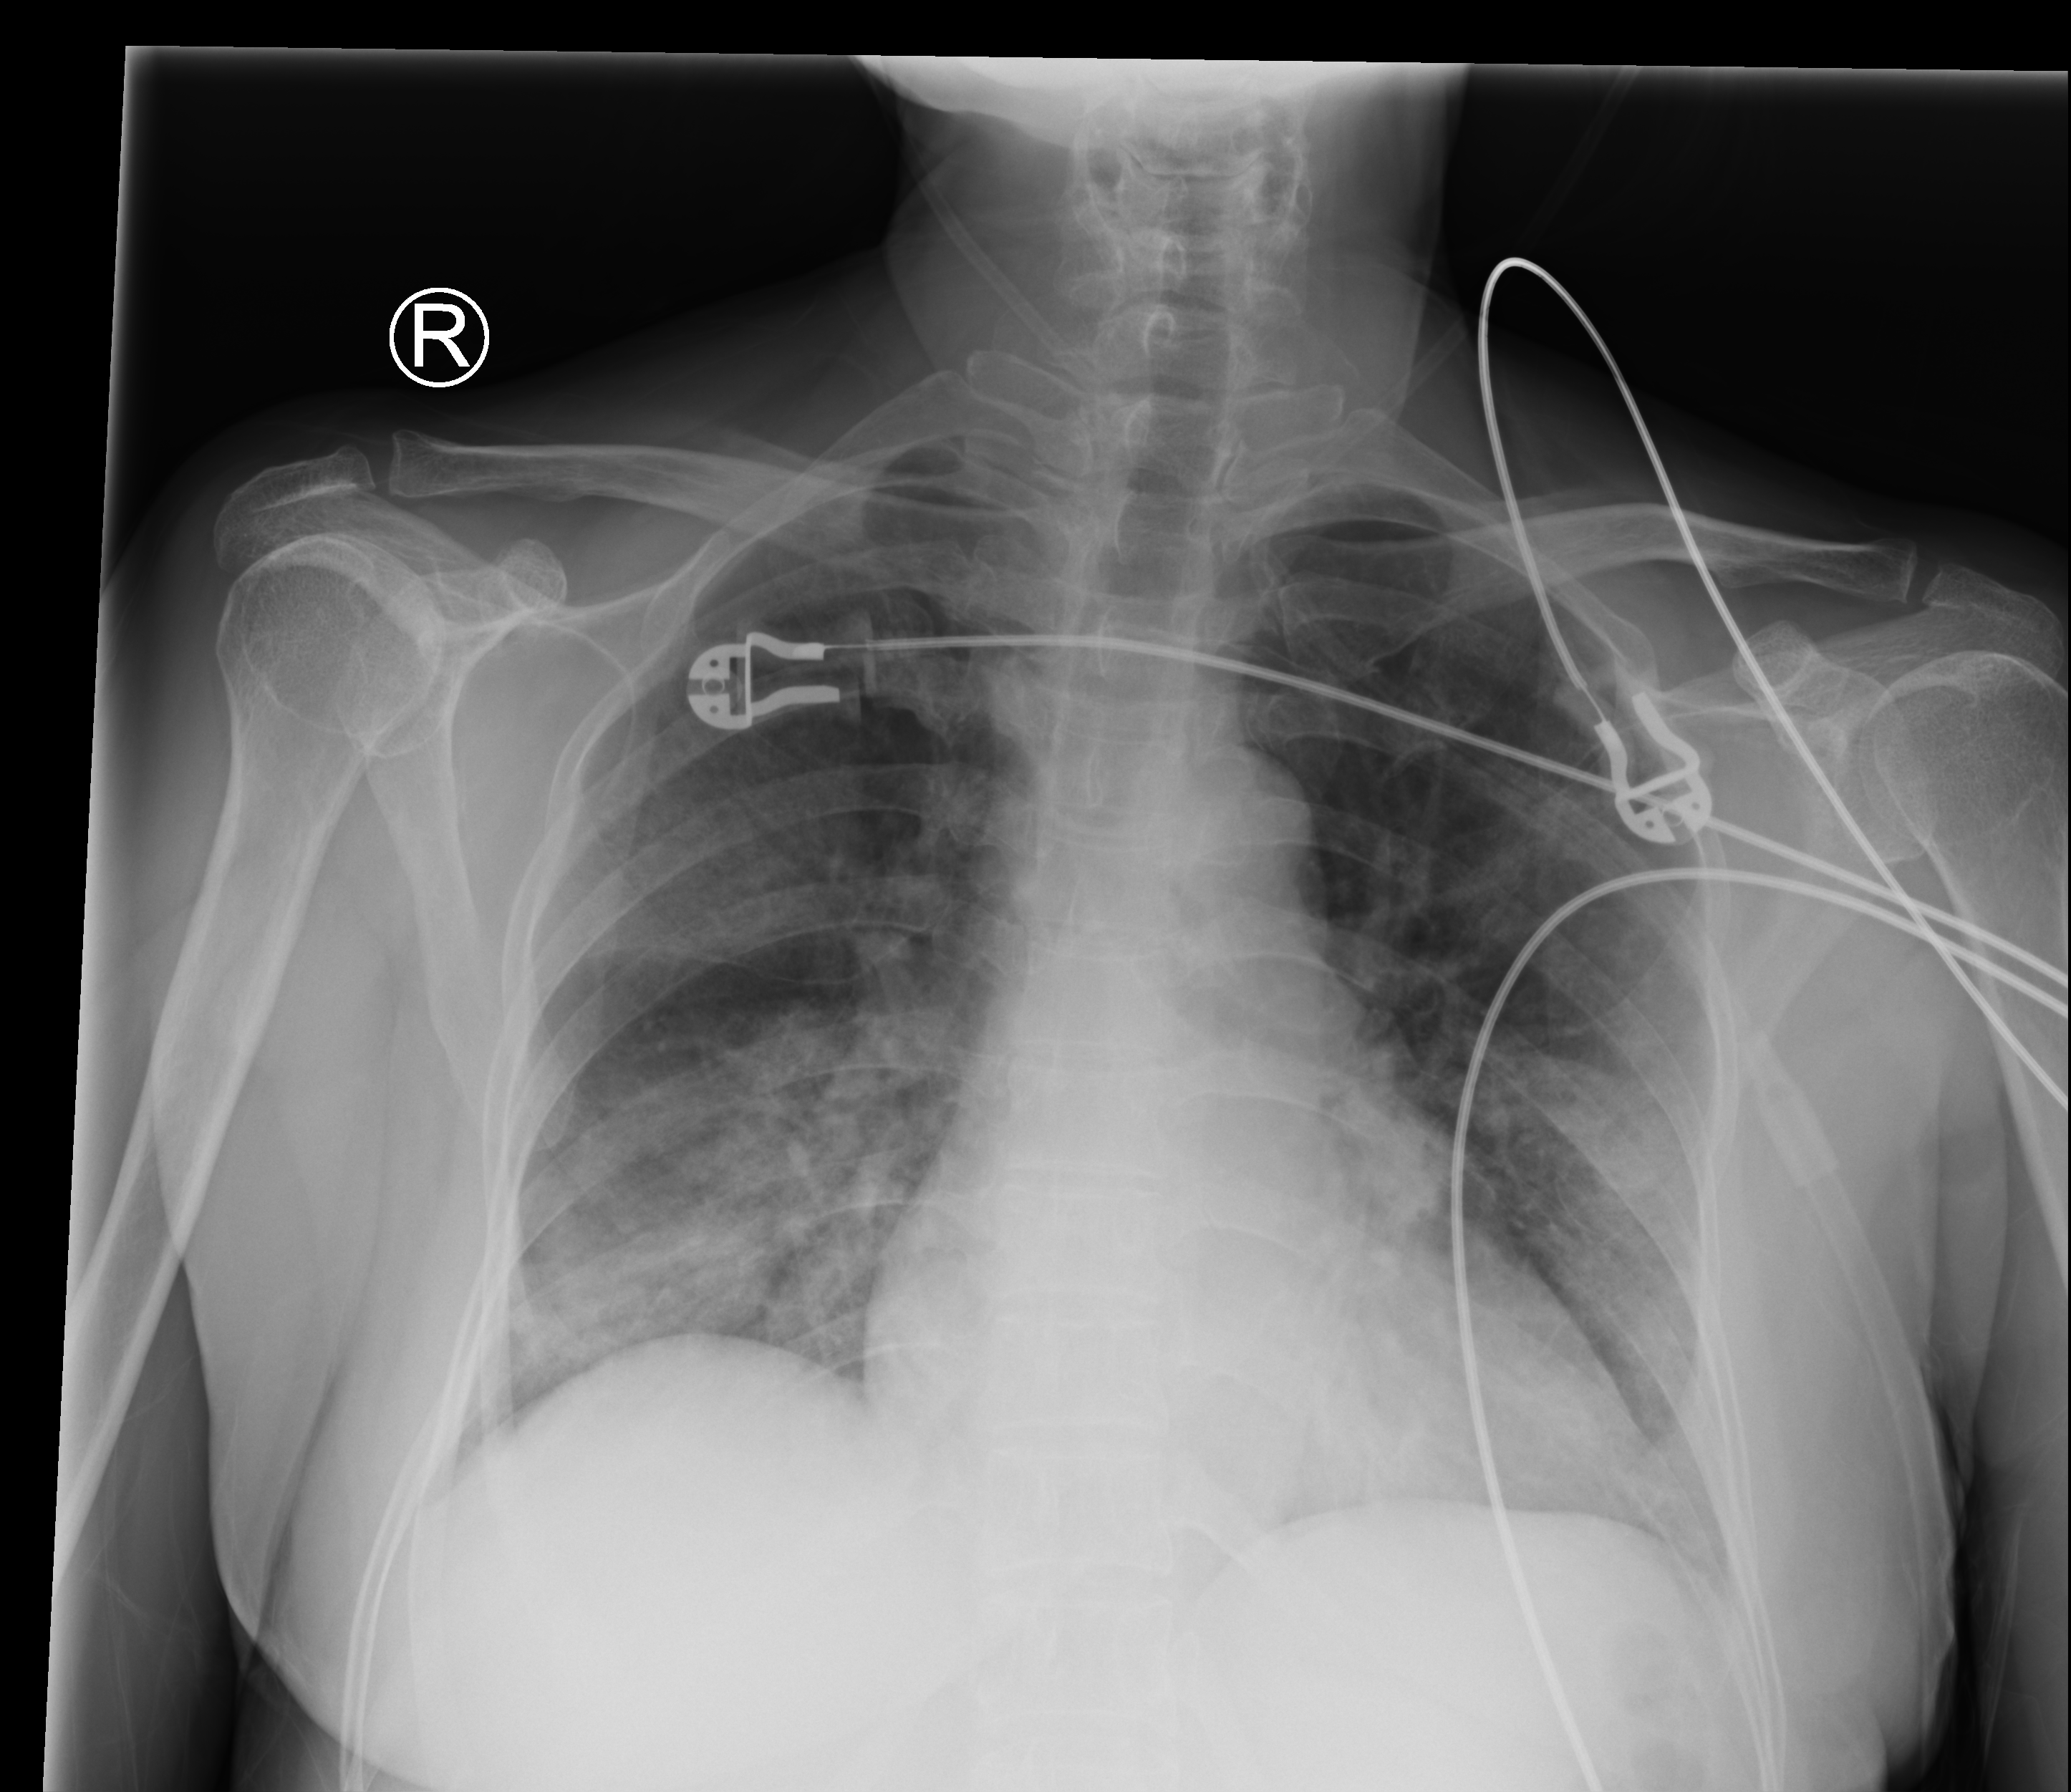
Portable chest radiograph, anteroposterior (AP) projection. Female patient hospitalised with COVID-19, age 60–74 years.
Admission-level facts for this patient (not findings on this image; timing relative to this image not recorded): COPD (admission record): no; admitted to intensive care during this hospital stay: yes.